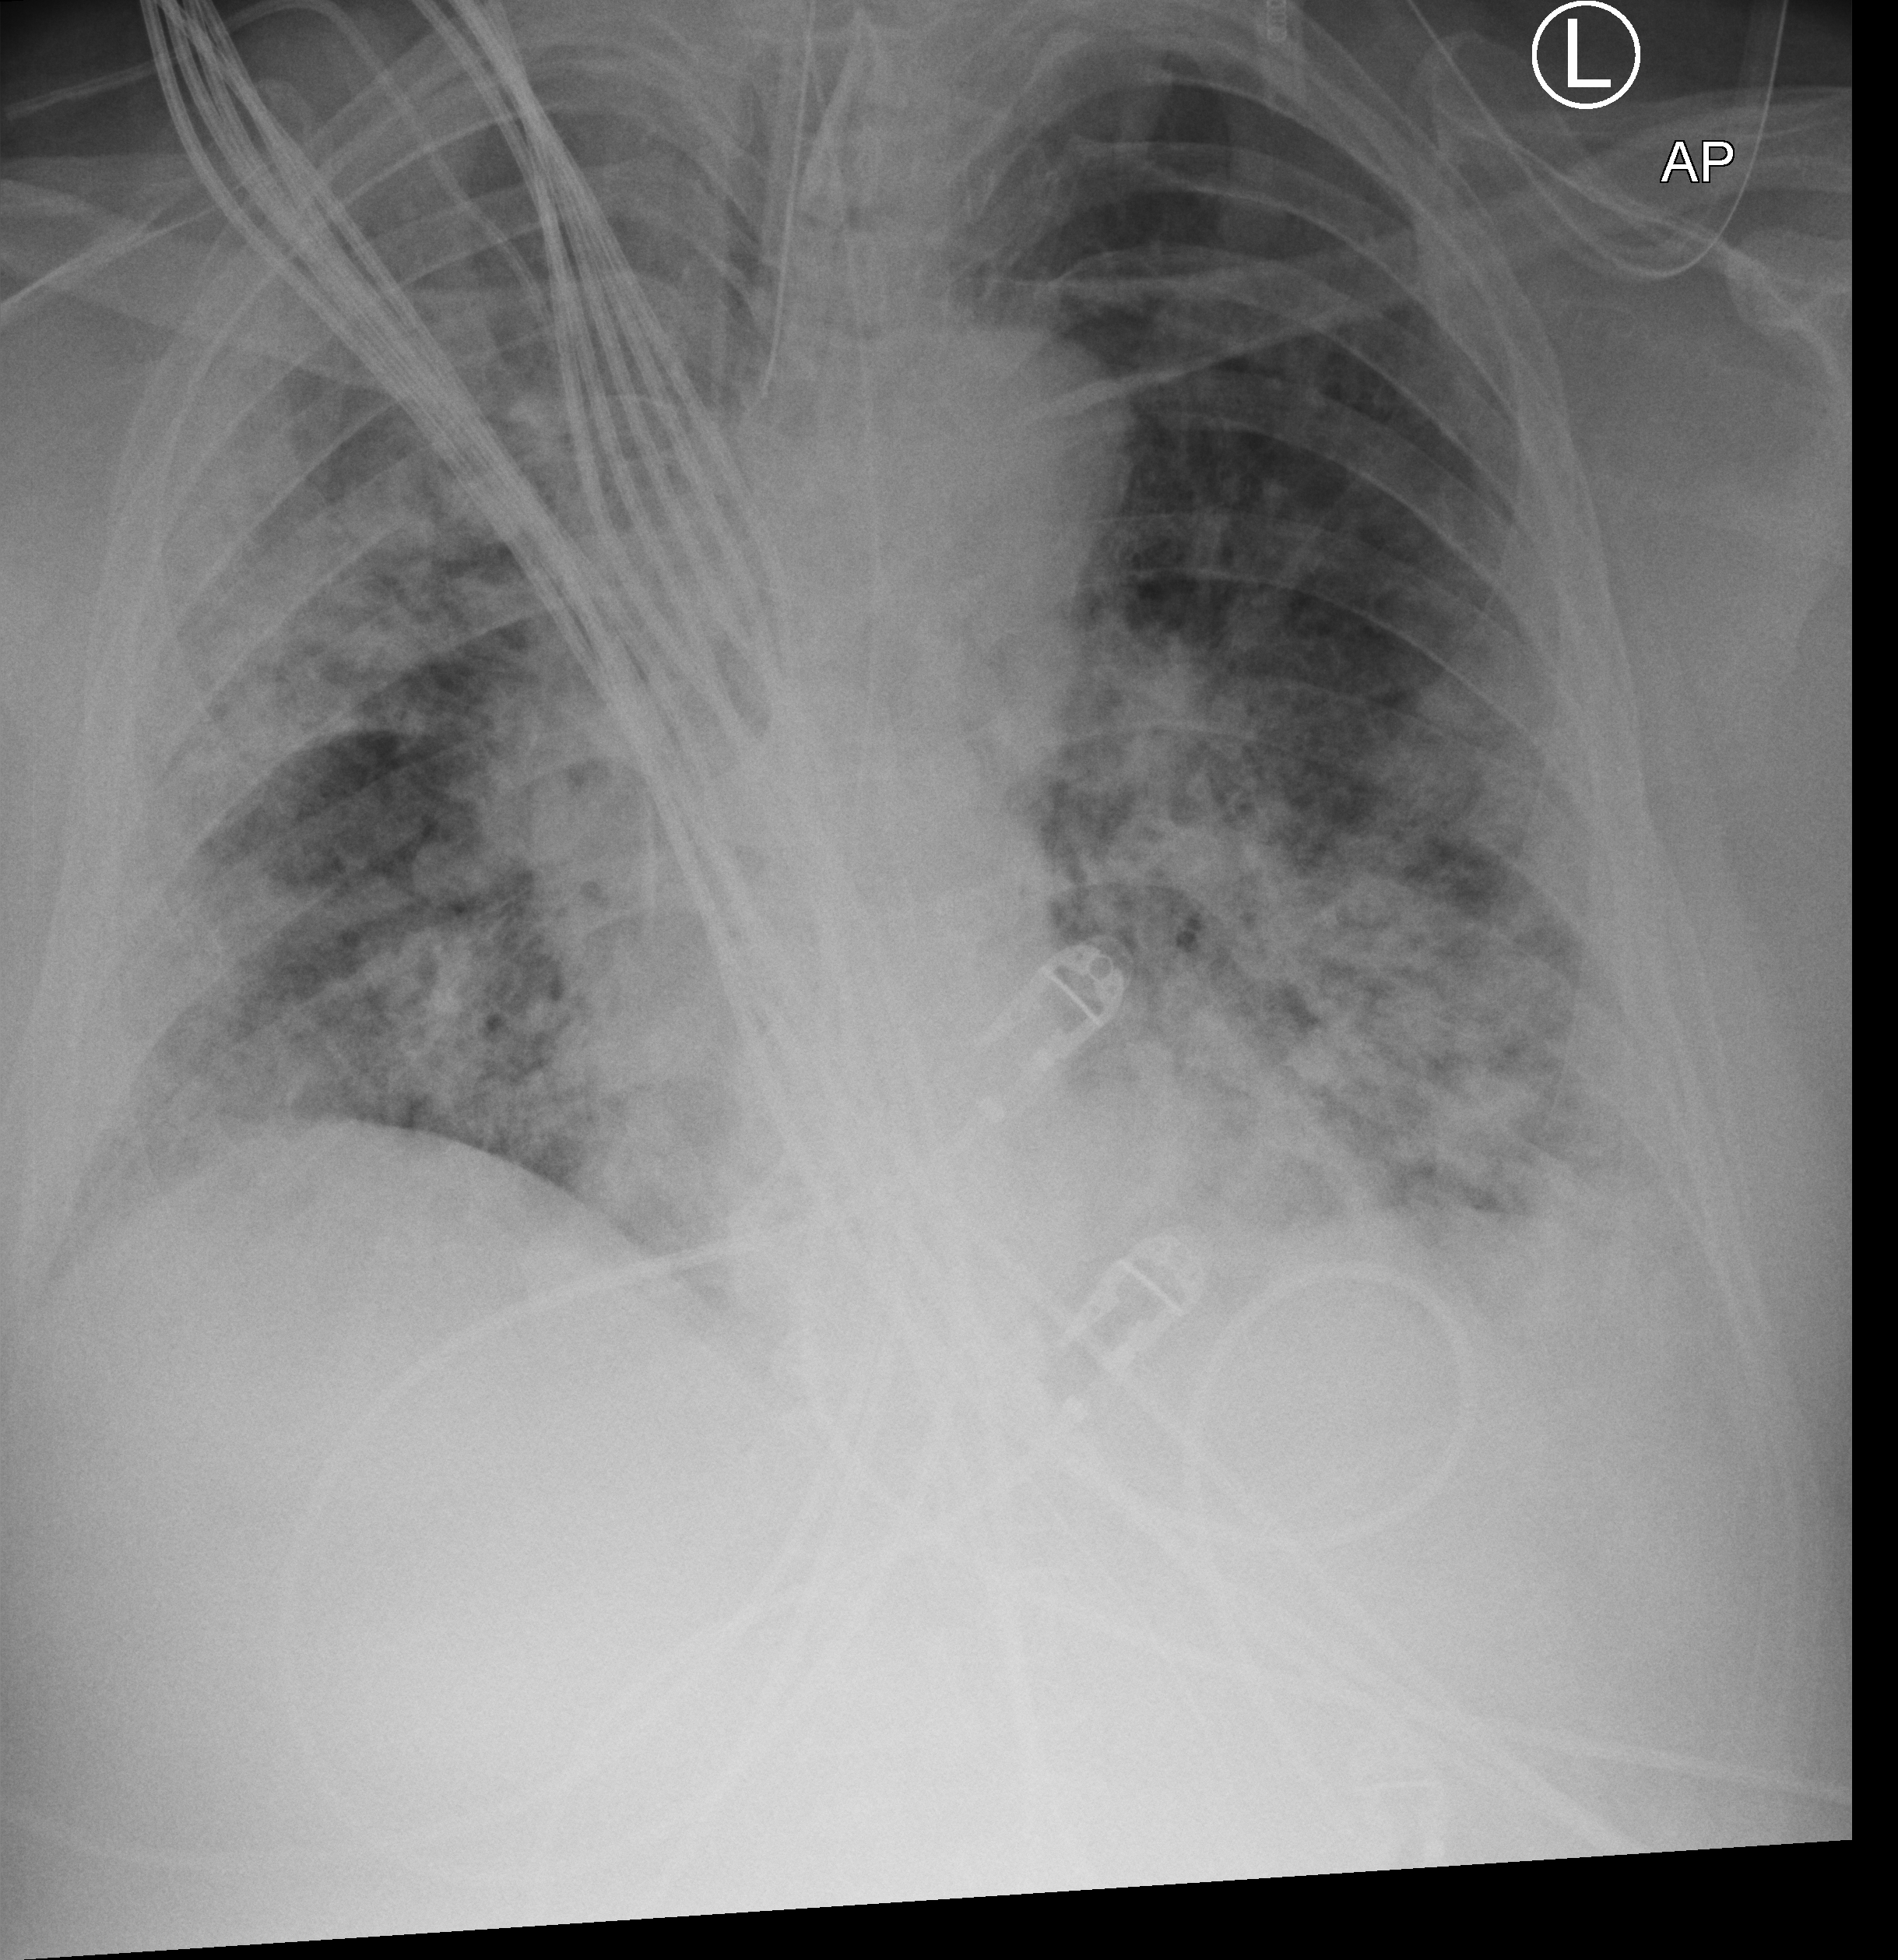
Portable chest radiograph, anteroposterior (AP) projection. Adult patient hospitalised with COVID-19, age 18–59 years.
From the hospital-stay record, not from the radiograph (when in the stay this image was taken is not recorded): COPD (admission record): no; length of hospital stay: 28 days.